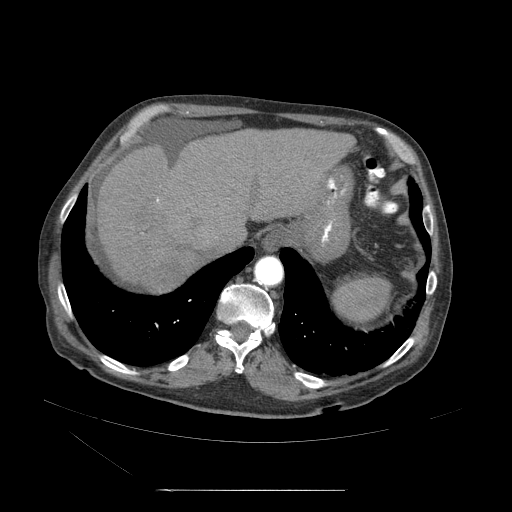
Contrast-enhanced abdominal CT (liver protocol), one axial slice. Soft-tissue window (W 400 / L 40 HU). 2.5 mm slice thickness. 512 × 512 image matrix. Case-level facts recorded for this patient, not image findings: diagnosis: hepatocellular carcinoma (patient treated with transarterial chemoembolisation; whether this scan precedes or follows treatment is not stated here); TNM stage (as recorded): Stage-II; Child-Pugh class: A; tumour nodularity: multinodular; tumour size: 1 cm.
Outlined on this slice (semi-automatic segmentation, software-assisted and operator-edited):
- abdominal aorta: bounding box (x1, y1, x2, y2) in pixels: (254, 256, 284, 288)
- liver parenchyma outside the tumour (the mass and vessels are separate outlines, so this box may not span the whole liver): (95, 131, 355, 290)
- mass: (143, 268, 186, 301)
- liver vessels: (106, 200, 236, 263)